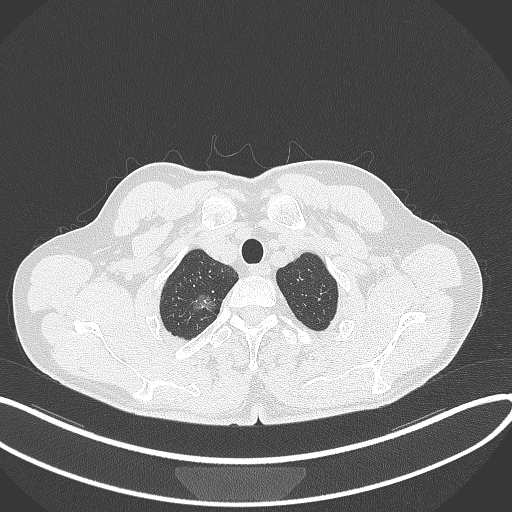
Chest CT, one axial slice. Slice 349 of 407 in the series (ordered by position). 120 kVp. Lung window (W 1500 / L -600 HU). 1 mm slice thickness. 512 × 512 image matrix, field of view 400 × 400 mm. Male patient, age 58 years. From the clinical record (not read from this slice): clinical TNM (as recorded): T1c N0 M0; histopathological grade: G1-2.
Structures marked on this image (bounding box drawn by a radiologist):
- lung tumour (recorded histology: adenocarcinoma): bounding box (x1, y1, x2, y2) in pixels: (187, 287, 222, 321)